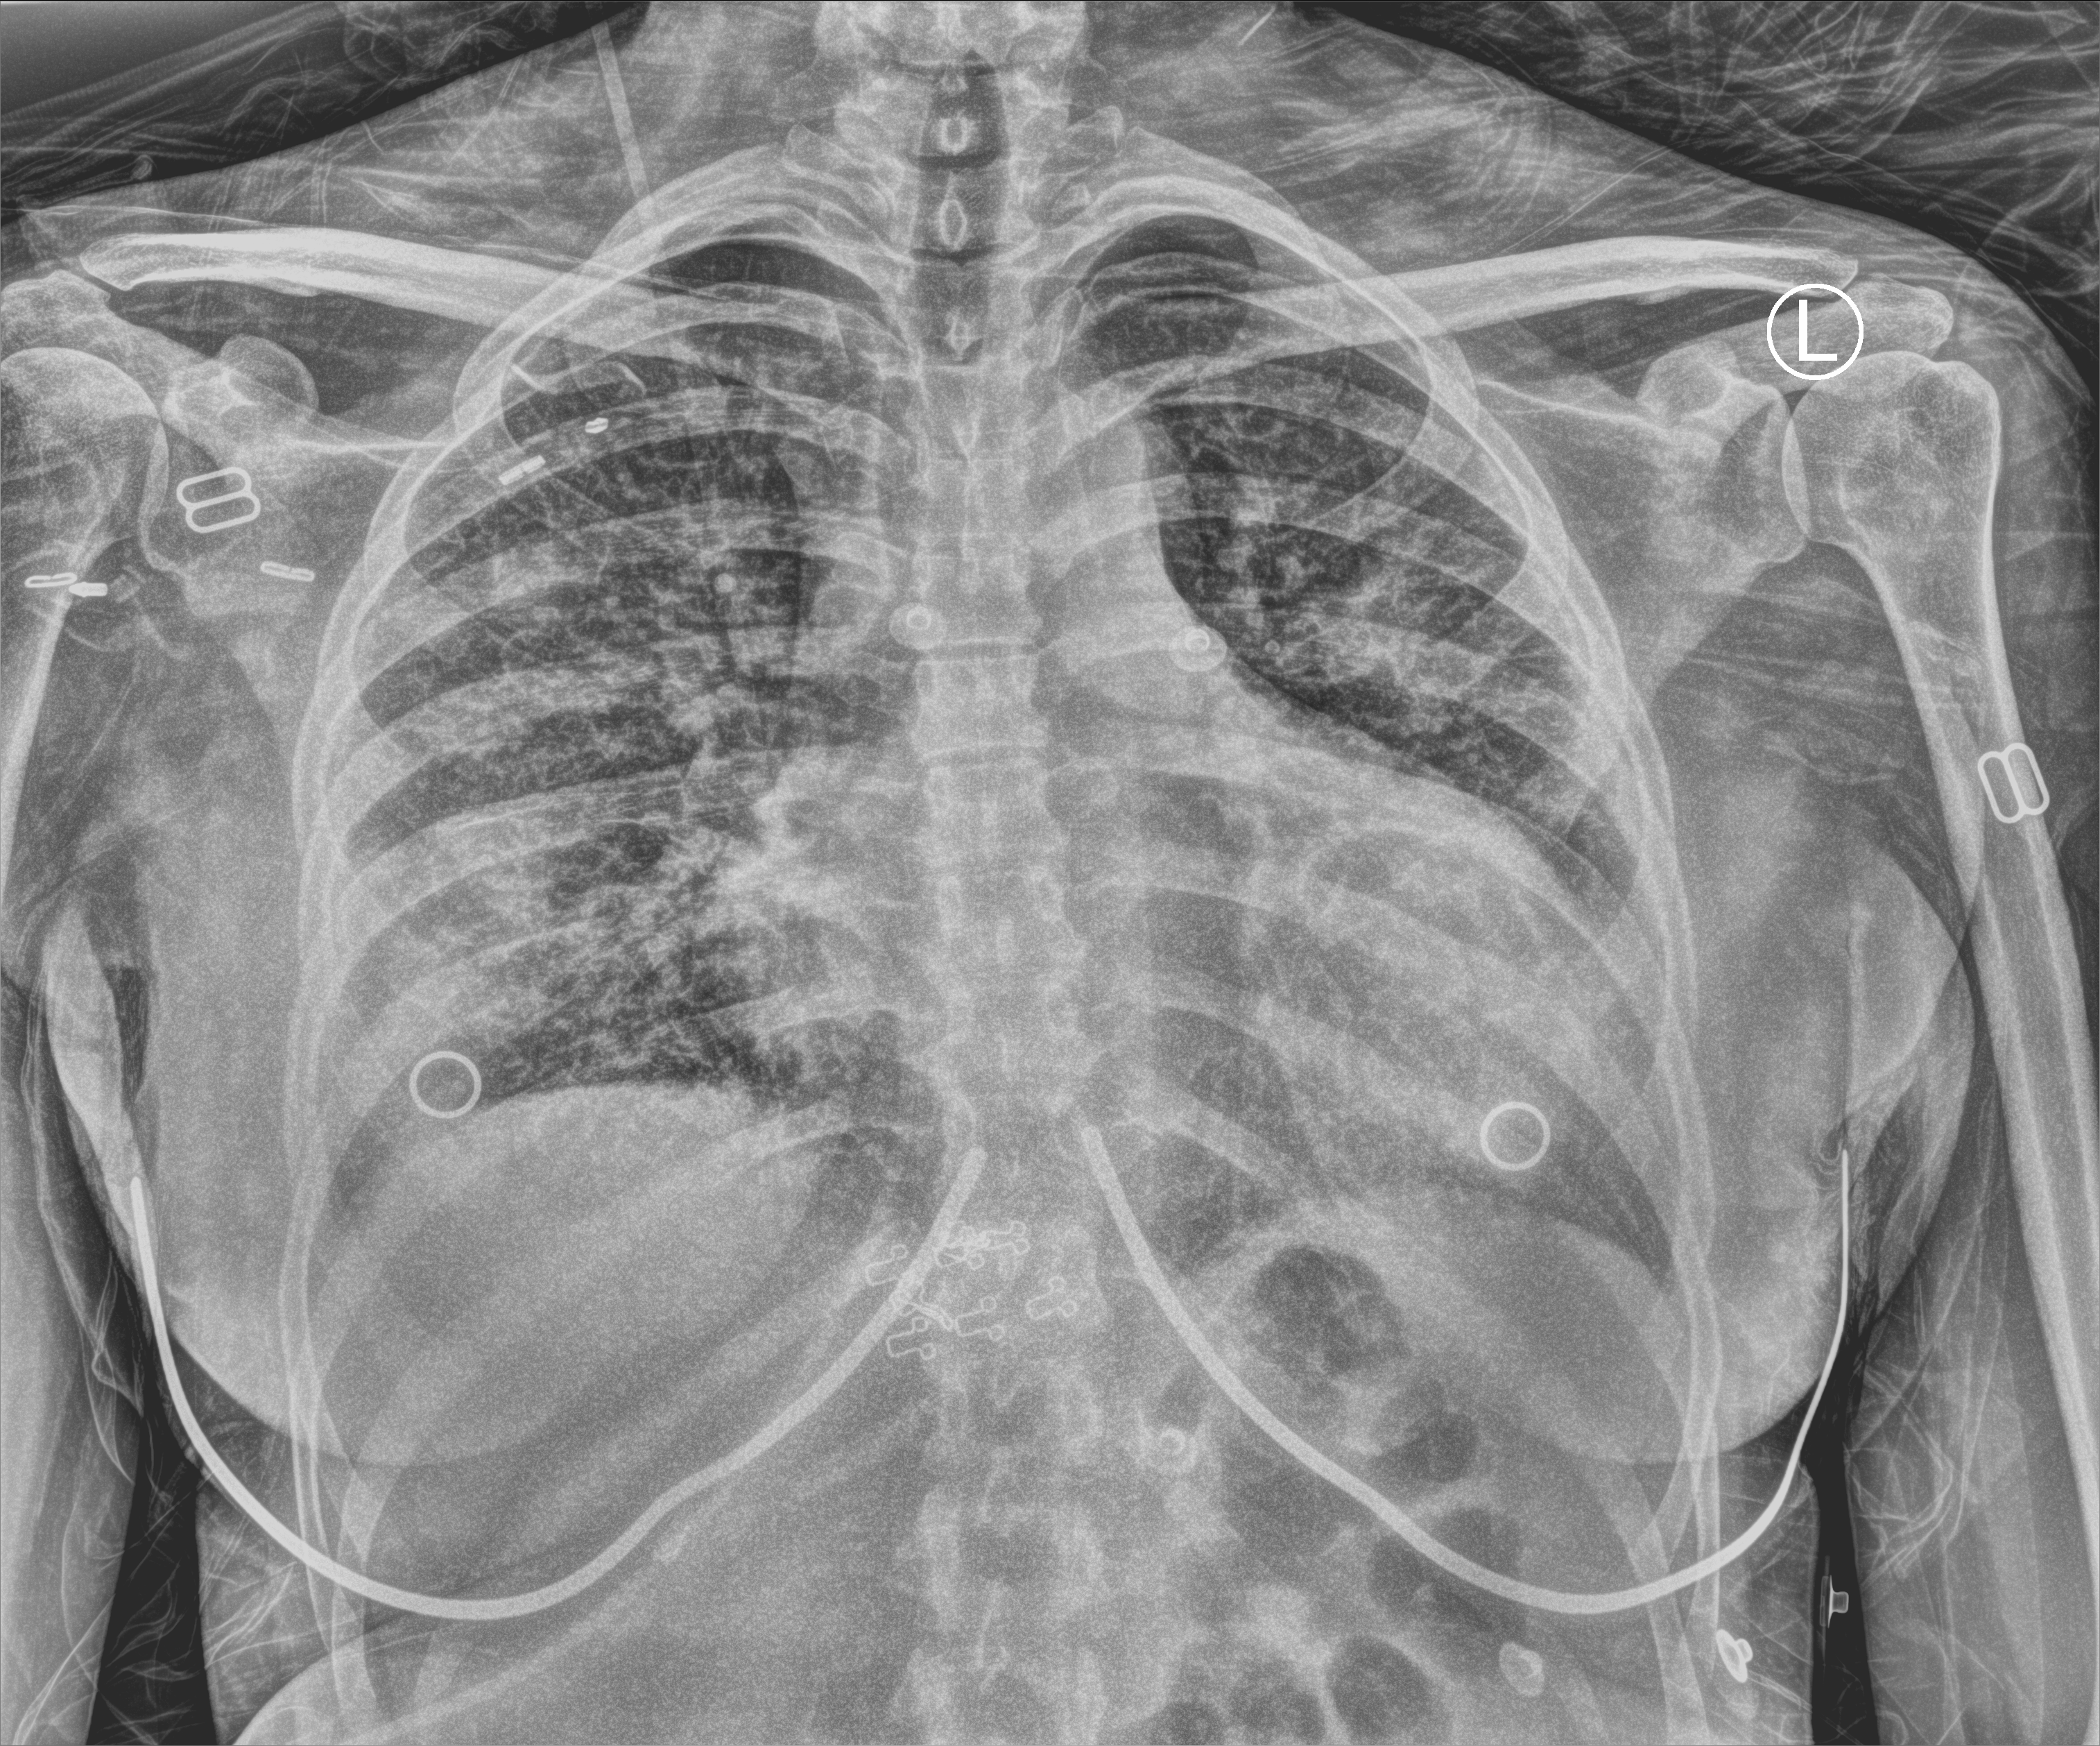
Chest X-ray (portable); anteroposterior (AP) projection. Female patient hospitalised with COVID-19, age 18–59 years.
From the hospital-stay record, not from the radiograph (when in the stay this image was taken is not recorded): admitted to intensive care during this hospital stay: no; mechanically ventilated during this hospital stay: no.